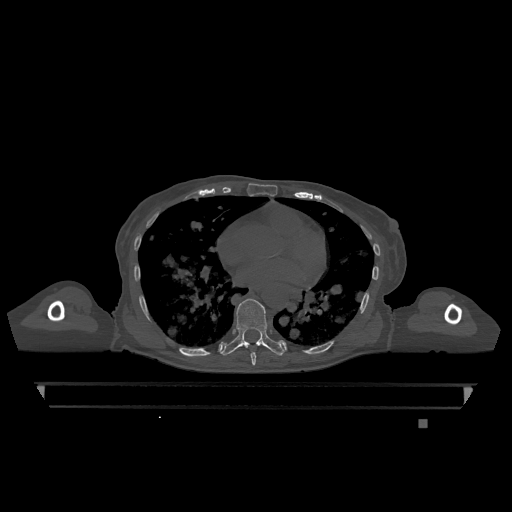
CT including the spine, one axial slice. Slice 702 of 1317 in the series (ordered by position). Bone window (W 1800 / L 400 HU). 0.5 mm slice thickness. 512 × 512 image matrix. Patient: female, 74 years. From the clinical record (not read from this slice): primary cancer: lung; vertebrae with lytic lesions (as recorded): T1, T4, T5, T6, L4, L5.
Annotated regions visible in this slice (semi-automatic segmentation, software-assisted and operator-edited):
- T7 vertebra: bounding box [x1, y1, x2, y2] px = [250, 352, 256, 366]
- T9 vertebra: [221, 298, 284, 356]